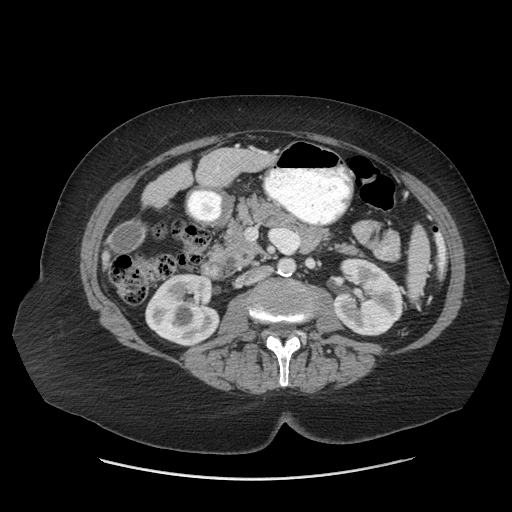
Contrast-enhanced abdominal CT (liver protocol), one axial slice; position 16 of 69 along the scan axis; reconstruction kernel STANDARD; soft-tissue window (W 400 / L 40 HU); 2.5 mm slice thickness; 512 × 512 image matrix, field of view 420 × 420 mm. Case-level facts recorded for this patient, not image findings: diagnosis: hepatocellular carcinoma (patient treated with transarterial chemoembolisation; whether this scan precedes or follows treatment is not stated here); TNM stage (as recorded): Stage-IIIB; Child-Pugh class: A; tumour differentiation: moderately differentiated.
Structures marked on this image (semi-automatically segmented with operator editing):
- liver parenchyma outside the tumour (the mass and vessels are separate outlines, so this box may not span the whole liver): bounding box [x1, y1, x2, y2] px = [102, 146, 275, 268]
- liver vessels: [210, 160, 220, 182]